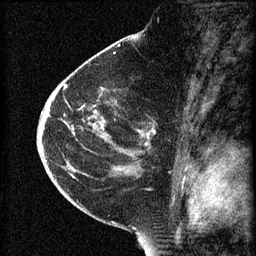
Breast MRI (dynamic contrast-enhanced), one sagittal slice. Slice 38 of 60 in the series (ordered by position). 3 images stored at this slice position (order not interpretable as contrast timing). 1.5 T. TE 4.2 ms, TR 8.2 ms. 2 mm slice thickness. 256 × 256 image matrix, field of view 180 × 180 mm. Patient: female, 44 years.
Structures marked on this image (semi-automatic segmentation, software-assisted and operator-edited):
- analysis volume of interest (the breast-tissue region the enhancement analysis was run in; not a lesion): bounding box (x1, y1, x2, y2) in pixels: (73, 86, 158, 165)
- tumour enhancement mask (voxels above the 70 % enhancement threshold inside the analysis volume of interest): (103, 124, 150, 139)